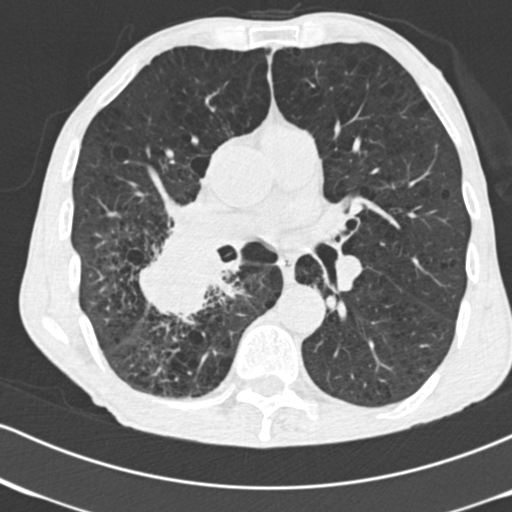
Low-dose screening chest CT, one axial slice; slice 90 of 182 in the series (ordered by position); reconstruction kernel B30f; 120 kVp; lung window (W 1500 / L -600 HU); 2 mm slice thickness; 512 × 512 image matrix.
Annotated regions visible in this slice (outlined manually by an expert reader):
- lesion 1 (tumor, lower lobe of right lung): box from (x=139, y=227) to (x=223, y=318) px